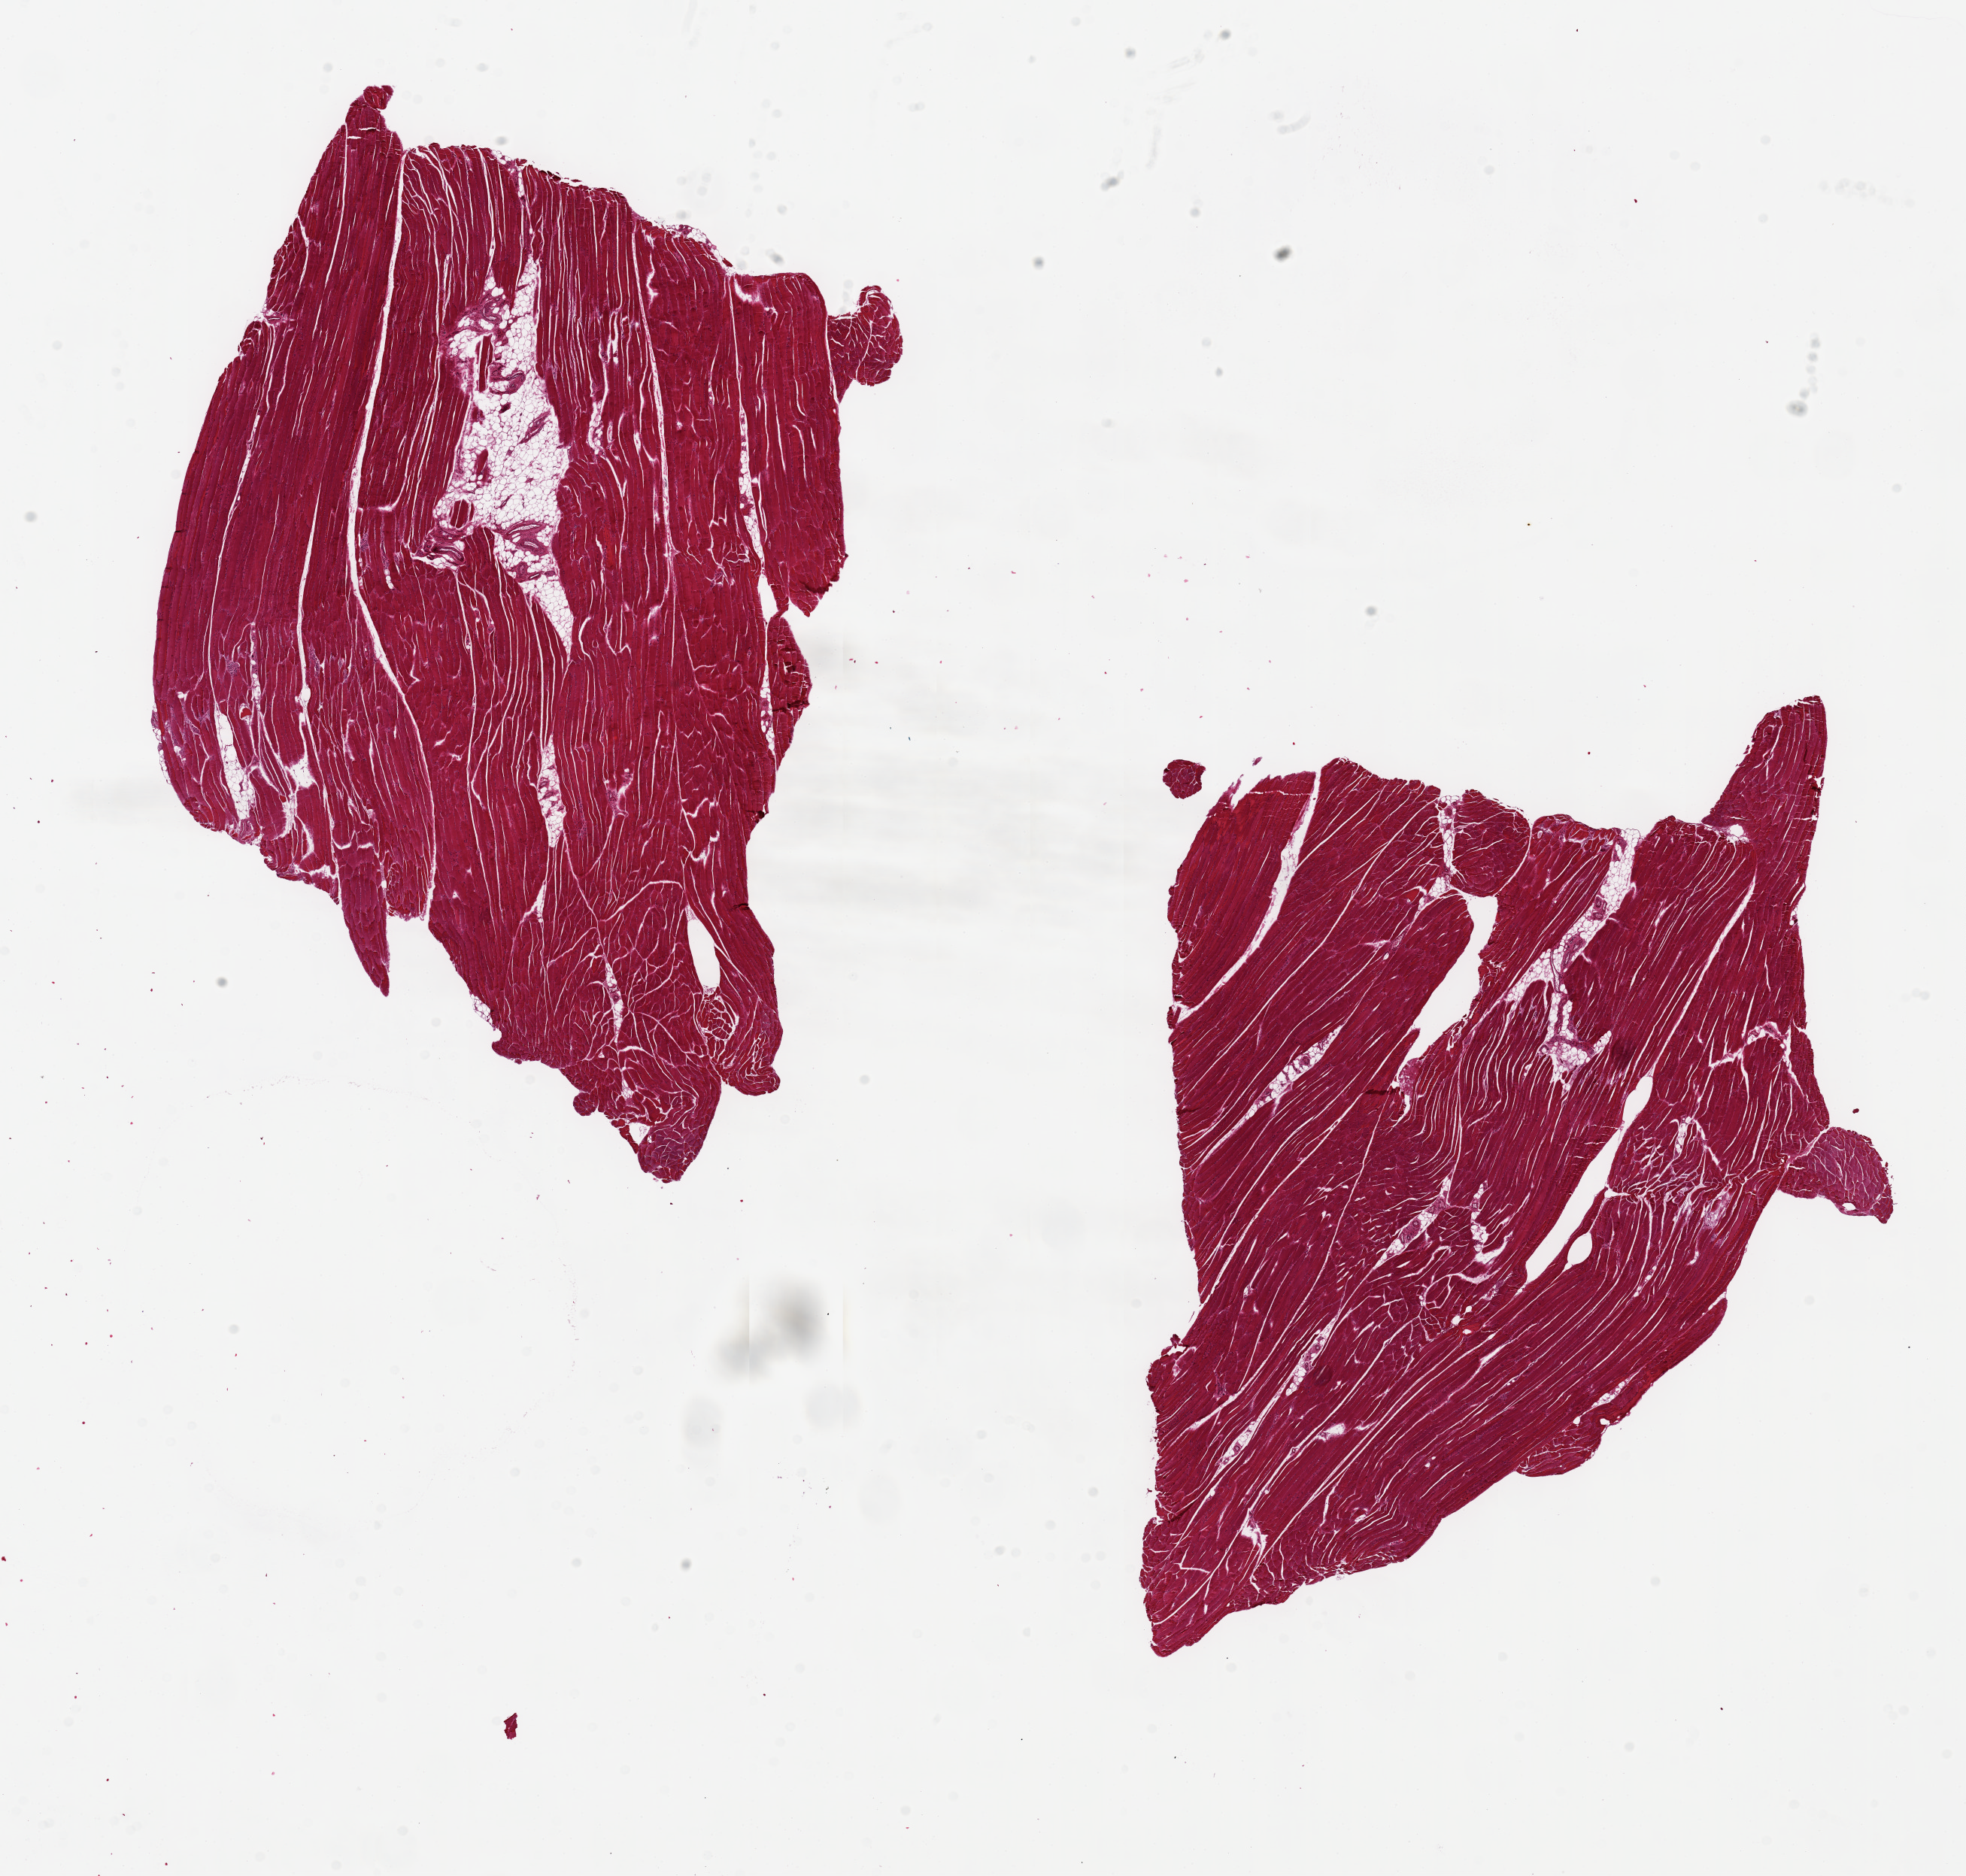
Haematoxylin and eosin whole-slide image — shown as a low-resolution overview of the whole scanned area (about 20.7 x 19.7 mm, slide scanned at 20x), PAXgene-fixed paraffin-embedded (PFPE) section, section of skeletal muscle (target tissue), donor tissue sample. Donor sex: female.
Reviewer comment on this tissue sample: 2 pieces. 9x8 7 9x9mm; 10% internal adipose in 1 piece.